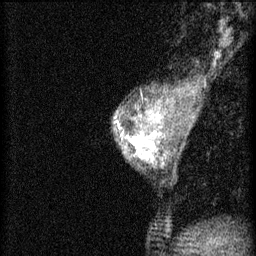
Breast MRI (dynamic contrast-enhanced), one sagittal slice; 3 images stored at this slice position (order not interpretable as contrast timing); 1.5 T; TE 4.2 ms, TR 8.2 ms; 2 mm slice thickness; 256 × 256 image matrix. Patient: female, 44 years.
Outlined on this slice (semi-automatic segmentation, software-assisted and operator-edited):
- analysis volume of interest (the breast-tissue region the enhancement analysis was run in; not a lesion): box from (x=112, y=128) to (x=156, y=171) px
- tumour enhancement mask (voxels above the 70 % enhancement threshold inside the analysis volume of interest): (x=121, y=130)–(x=156, y=163)